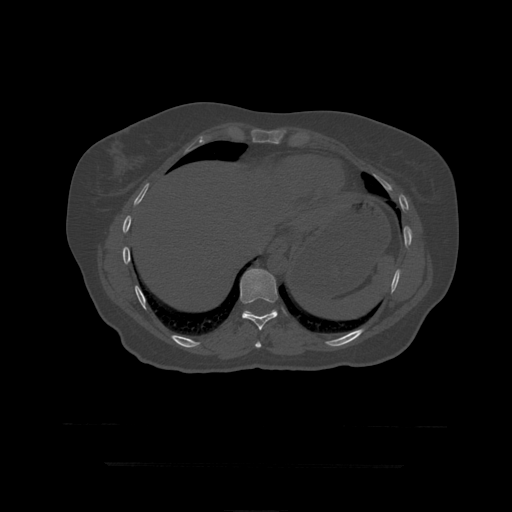
CT including the spine, one axial slice. Slice 238 of 399 in the series (ordered by position). Bone window (W 1800 / L 400 HU). 512 × 512 image matrix, field of view 450 × 450 mm. Patient age 41 years. From the clinical record (not read from this slice): primary cancer: breast.
Structures marked on this image (semi-automatically segmented with operator editing):
- T10 vertebra: bounding box [x1, y1, x2, y2] px = [241, 269, 278, 331]
- T11 vertebra: [243, 310, 278, 314]
- T9 vertebra: [255, 341, 262, 348]